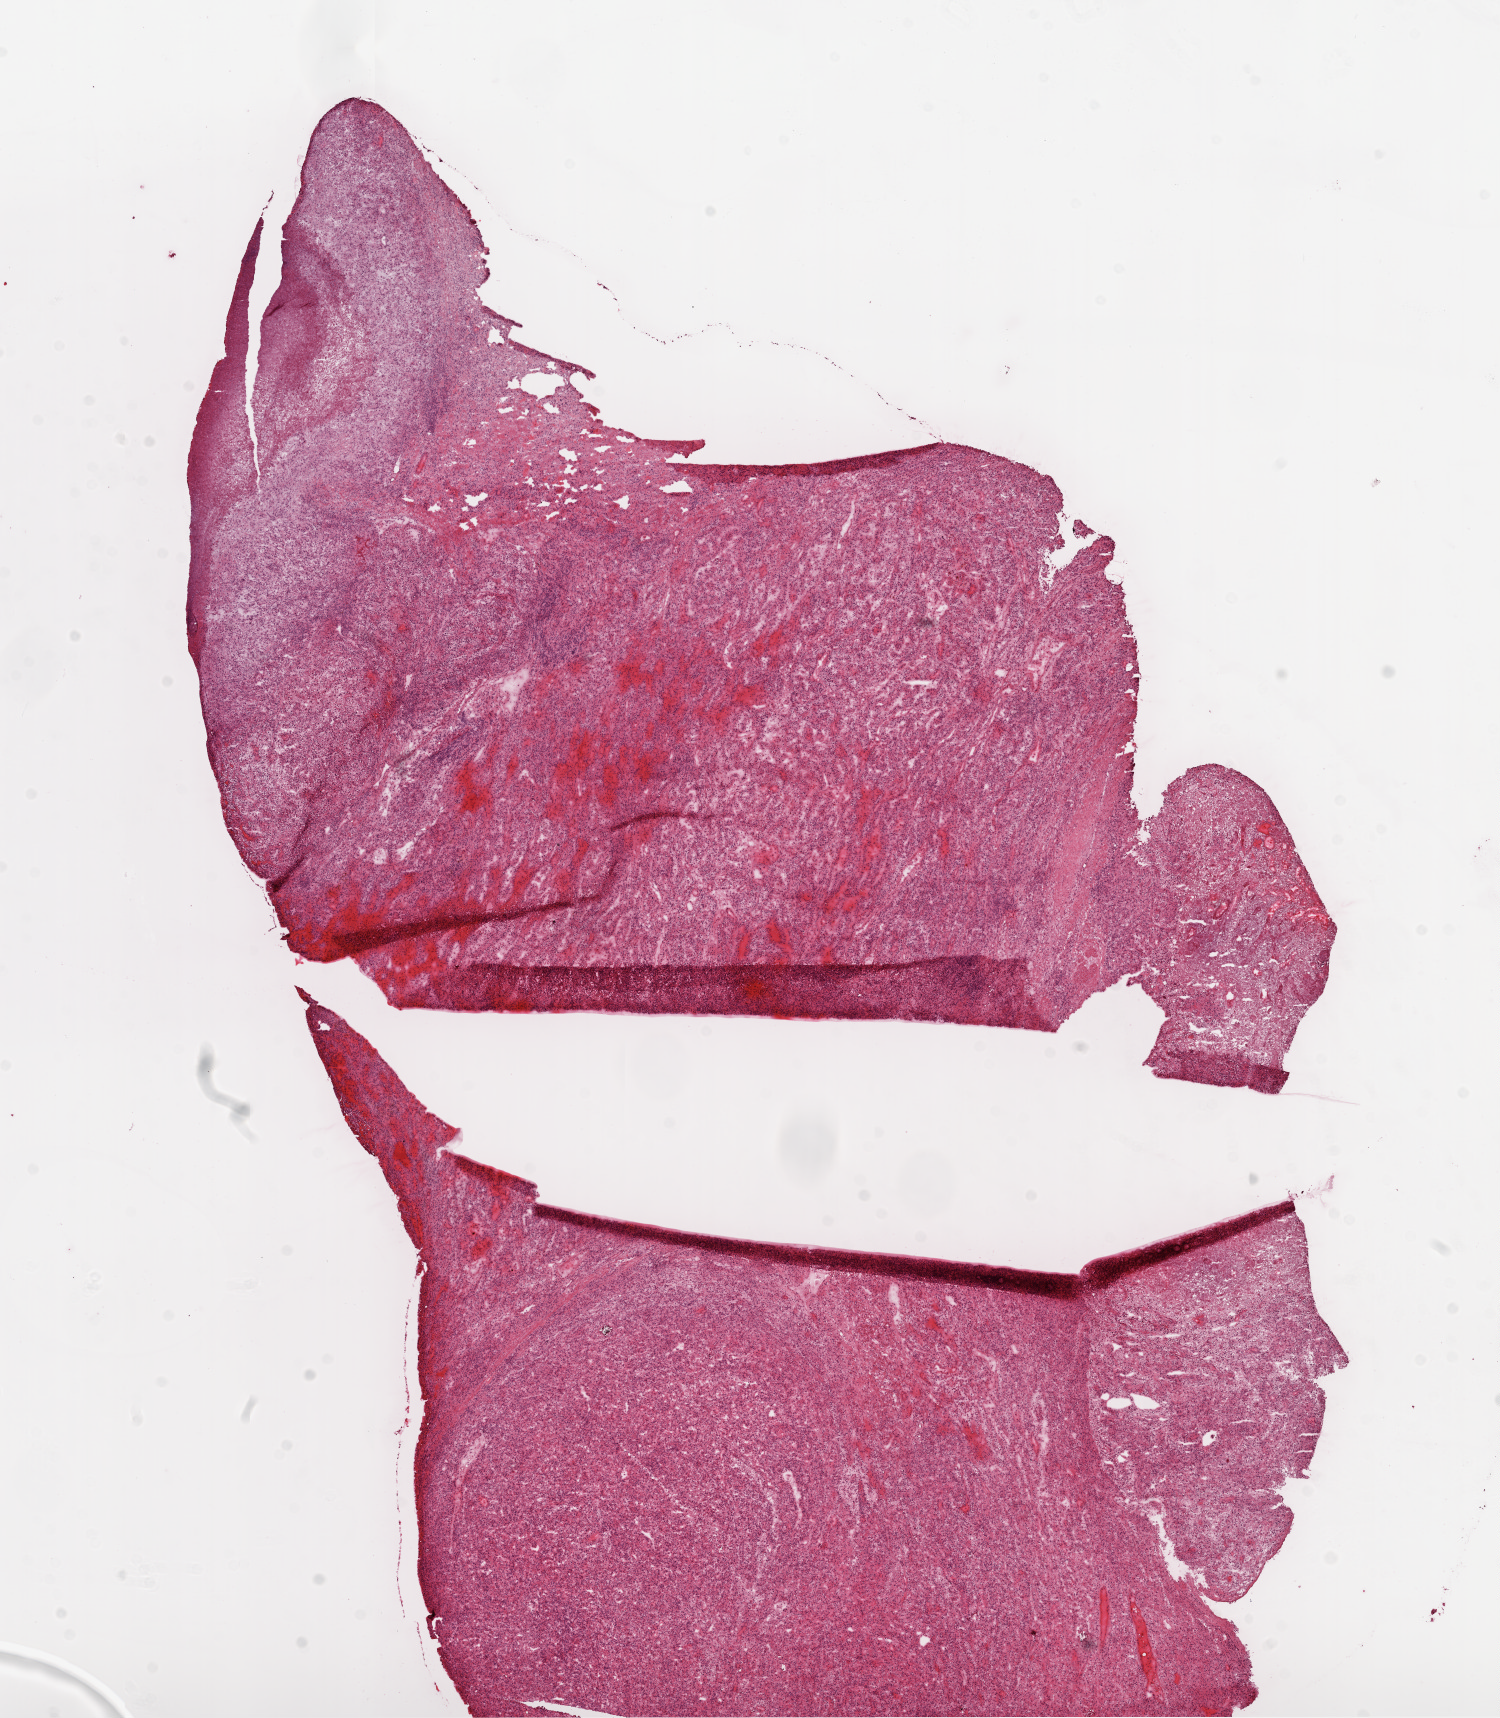
Digitized Hematoxylin and eosin (H&E) stained tissue section (whole slide), a low-resolution overview of the entire scanned area, about 12.0 x 13.8 mm. Frozen section. Primary tumour sample from the kidney. Male patient; age at initial diagnosis 62 years. Histologic grade: G4 (undifferentiated). Slide review estimates, as recorded: tumour cells 95%, tumour nuclei 90%, necrosis 5%. Infiltration values recorded for this section: lymphocyte infiltration 5%.
AJCC pathologic stage: IV. Pathologic diagnosis: Clear cell adenocarcinoma, NOS. Lymph nodes positive (case pathology): 0 of 5 examined.